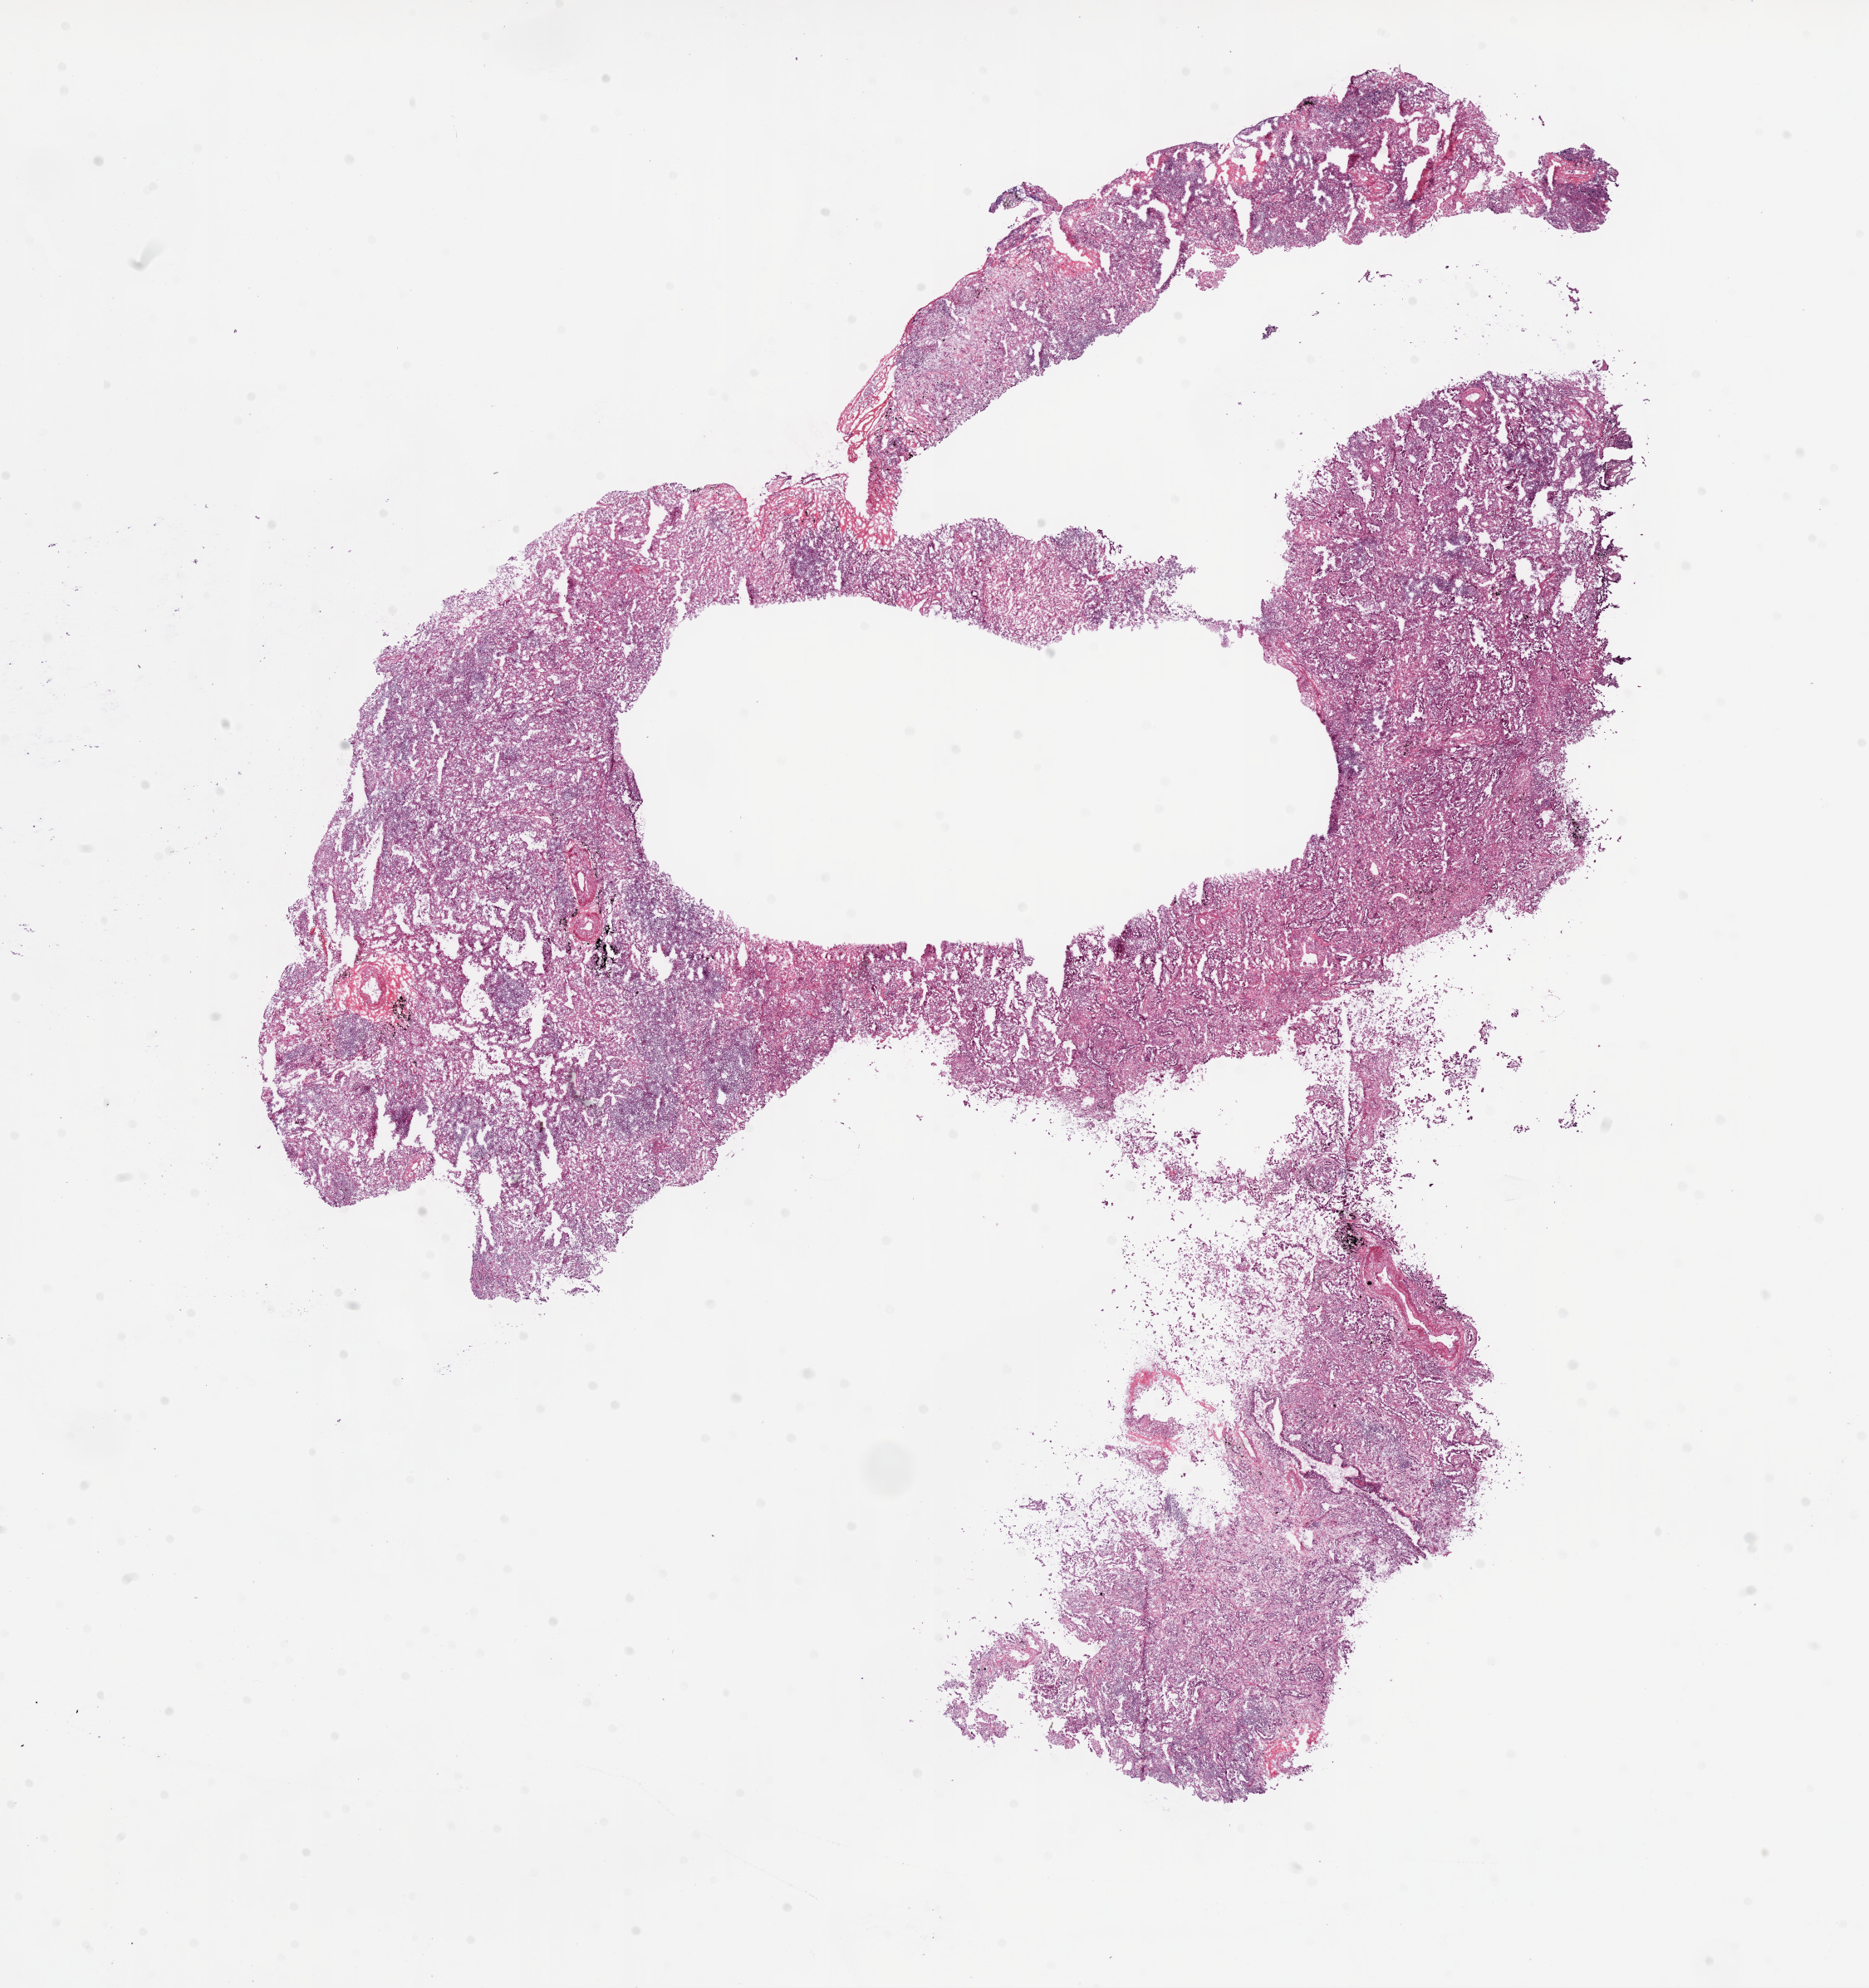
Digitized H&E-stained tissue section (whole slide), low-resolution overview of the scanned area, about 18.1 x 19.2 mm, frozen section from the bottom of the tissue portion, sample: primary tumour, lung. Female patient; age at initial diagnosis 79 years. Composition of this section per pathologist review: tumour cells 45%, tumour nuclei 35%, normal cells 40%, stromal cells 15%, necrosis 0%.
Histologic diagnosis: Adenocarcinoma with mixed subtypes (lower lobe, lung). AJCC pathologic stage: IIA. TNM: T1 N1 M0.